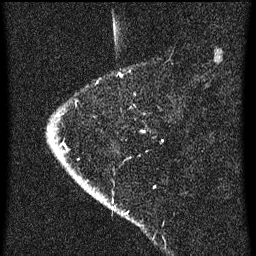
Breast MRI (dynamic contrast-enhanced), one sagittal slice; slice 10 of 60 in the series (ordered by position); dynamic contrast-enhanced series, image 2 of 3 at this slice position (ordered by acquisition); 1.5 T; TE 4.2 ms, TR 8 ms; 2 mm slice thickness; 256 × 256 image matrix, field of view 180 × 180 mm. Patient: female, 47 years.
Annotated regions visible in this slice (semi-automatic segmentation, software-assisted and operator-edited):
- analysis volume of interest (the breast-tissue region the enhancement analysis was run in; not a lesion): bounding box <46,76,165,193> (left, top, right, bottom; pixels)
- tumour enhancement mask (voxels above the 70 % enhancement threshold inside the analysis volume of interest): <48,128,61,147>